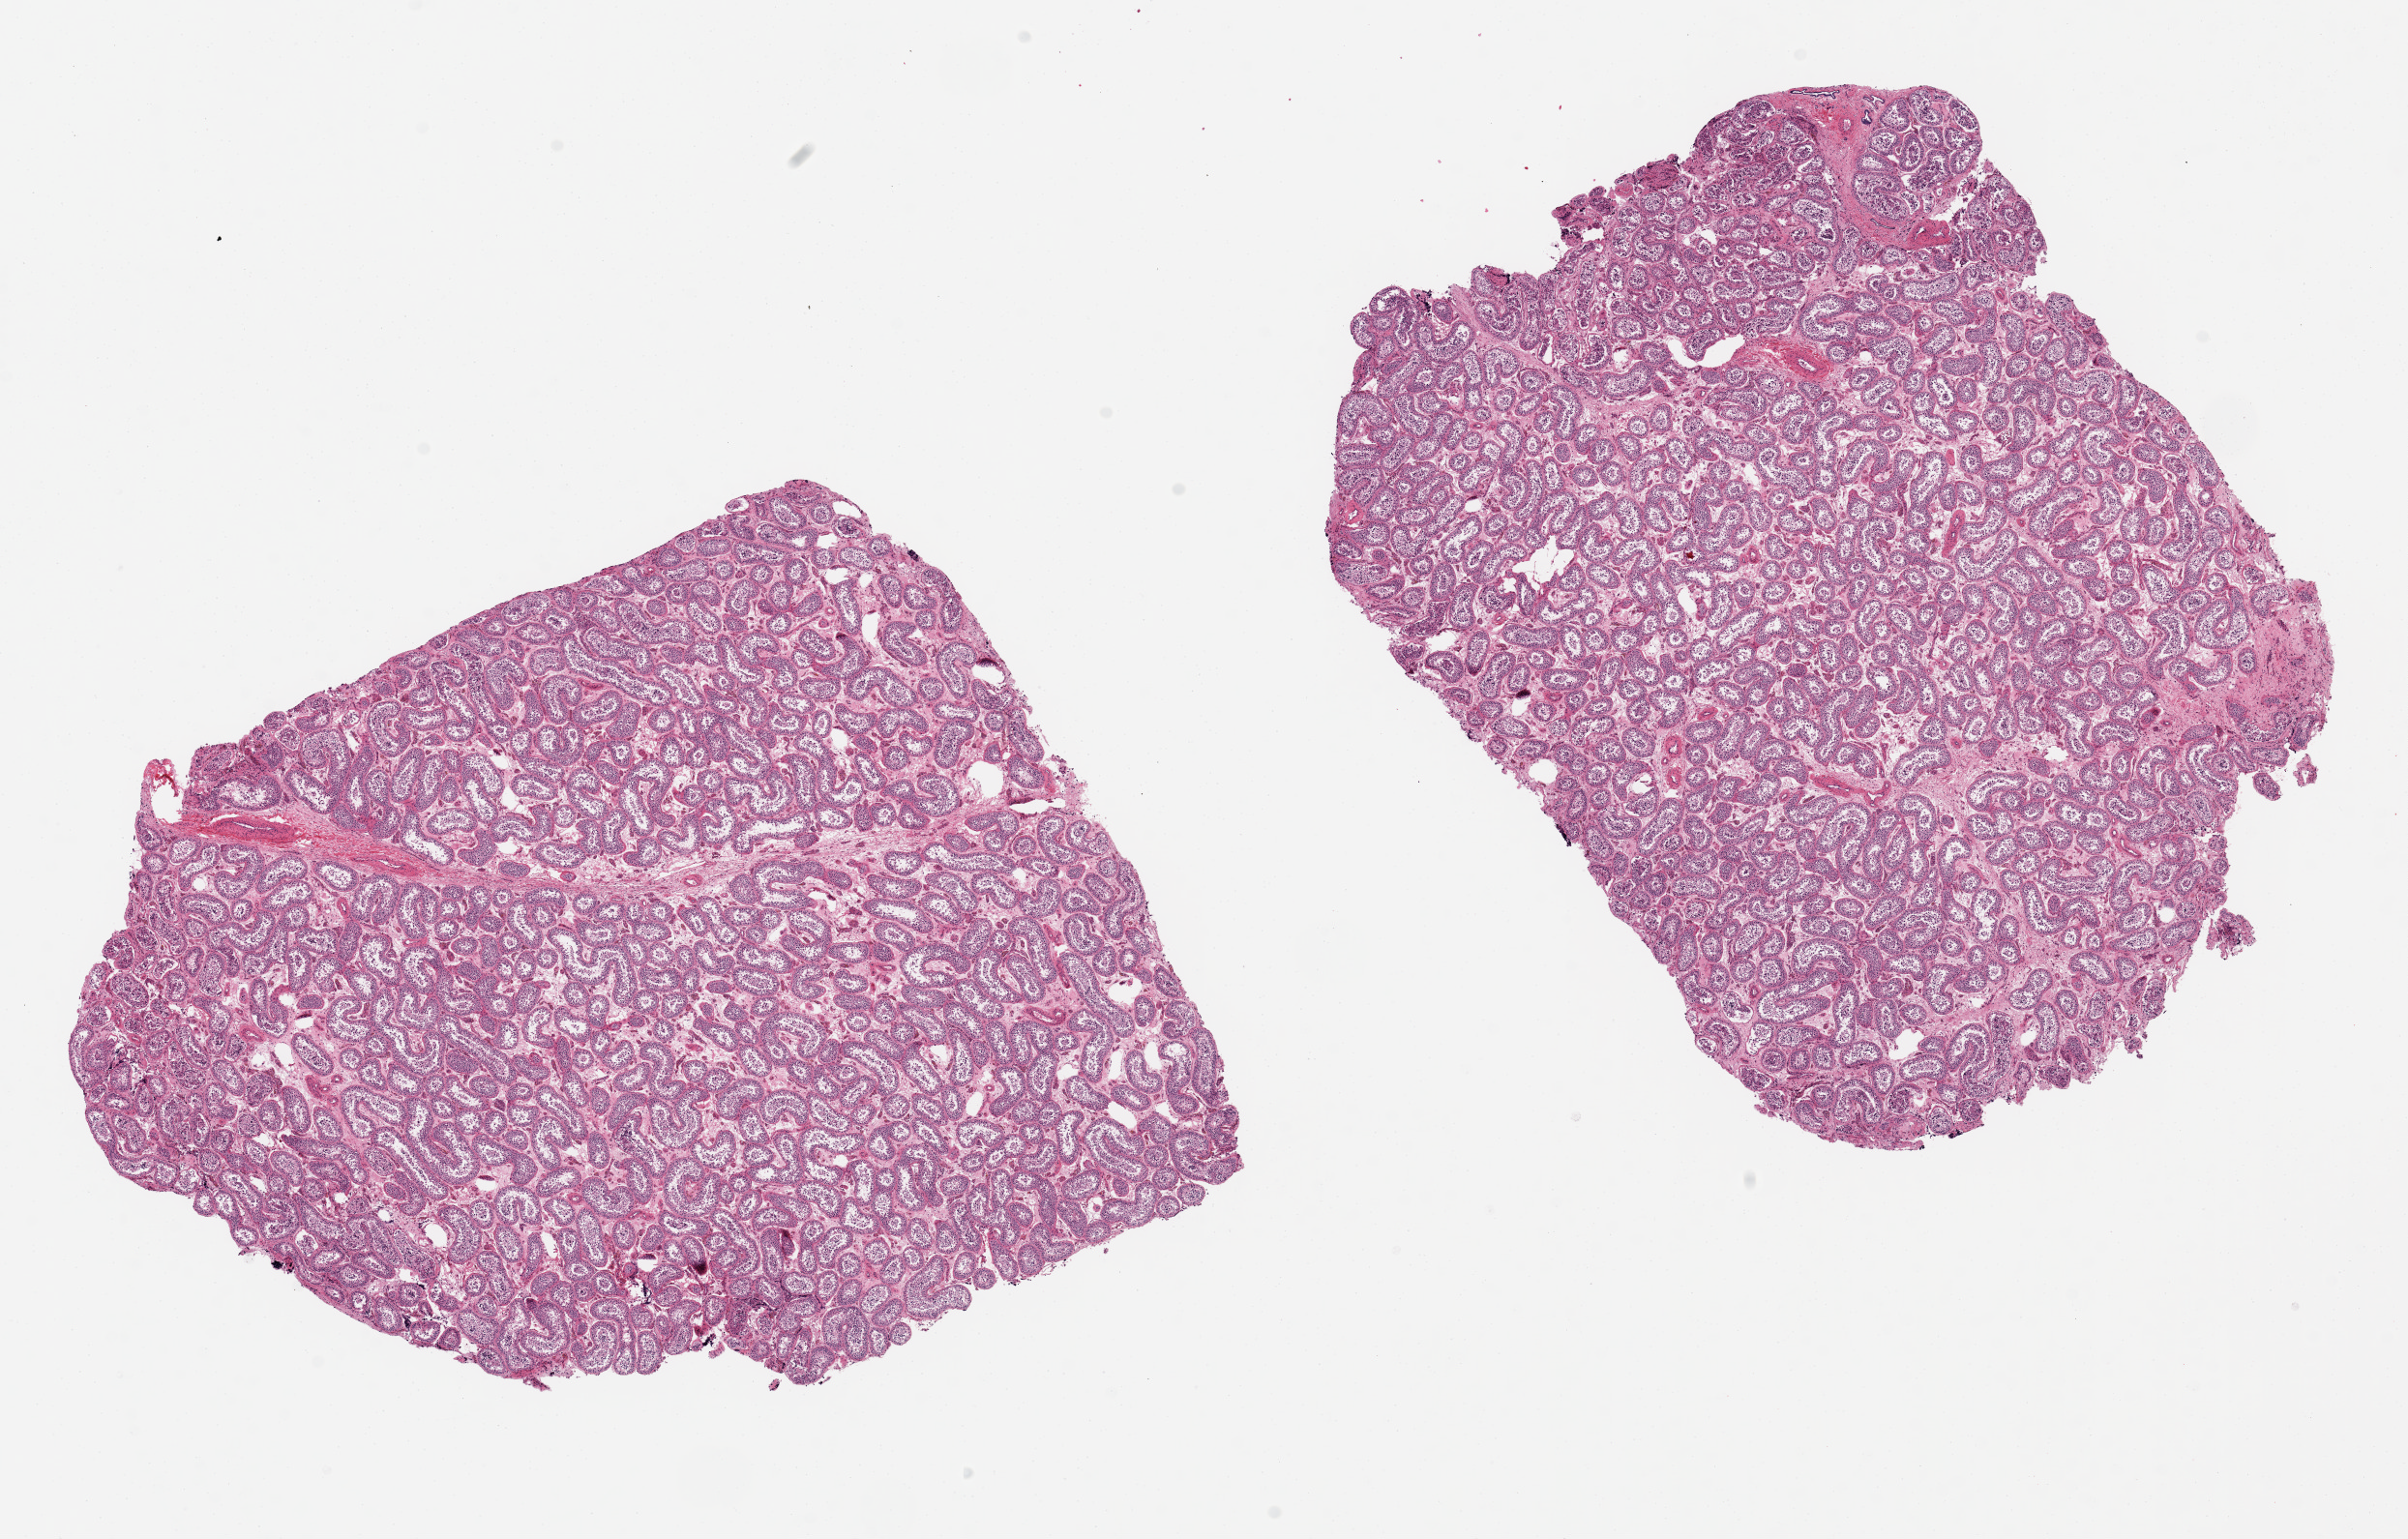
Hematoxylin and eosin (H&E) whole-slide image — a low-resolution overview of the entire scanned area, about 19.7 x 12.6 mm (from a 20x scan); PAXgene-fixed, paraffin-embedded tissue; target tissue: testis; tissue donor sample. Donor sex: male.
* pathologist's review note for this sample: 2 pieces, 8x6 & 8x7 mm; good spermatogenesis